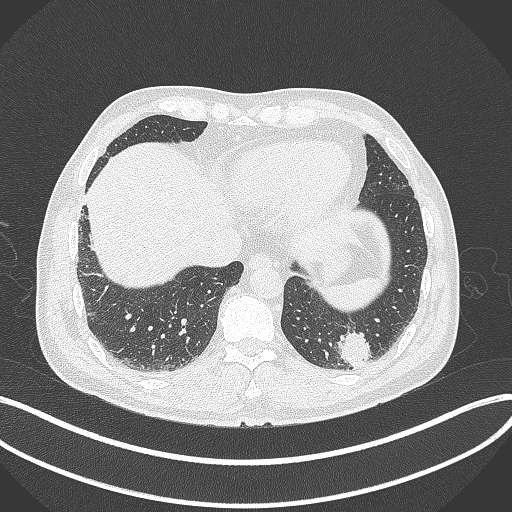
Chest CT, one axial slice. Slice 62 of 300 in the series (ordered by position). Reconstruction kernel B70f. 120 kVp. Lung window (W 1500 / L -600 HU). 1 mm slice thickness. 512 × 512 image matrix, field of view 400 × 400 mm. Patient: male, 54 years. Case-level facts recorded for this patient, not image findings: clinical TNM (as recorded): T1c N0 M1.
Annotated regions visible in this slice (bounding box drawn by a radiologist):
- lung tumour (recorded histology: adenocarcinoma): bounding box [x1, y1, x2, y2] px = [333, 325, 373, 369]